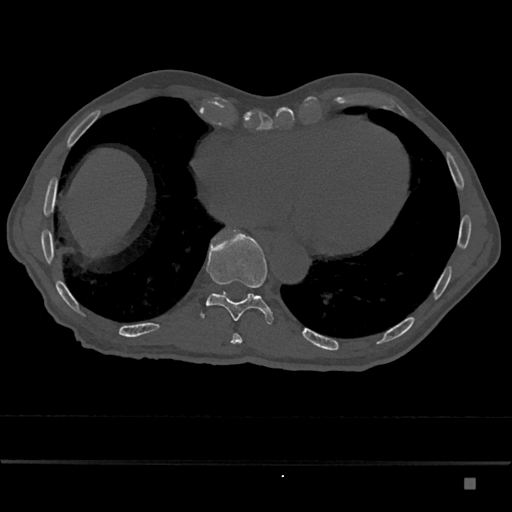
CT including the spine, one axial slice; position 739 of 797 along the scan axis; reconstruction kernel Br40s/3; 120 kVp; bone window (W 1800 / L 400 HU); 0.5 mm slice thickness; 512 × 512 image matrix. Male patient, age 72 years. Case-level facts recorded for this patient, not image findings: primary cancer: prostate.
Annotated regions visible in this slice (semi-automatic segmentation, software-assisted and operator-edited):
- T10 vertebra: box from (x=201, y=230) to (x=273, y=324) px
- T9 vertebra: (x=231, y=333)–(x=242, y=344)